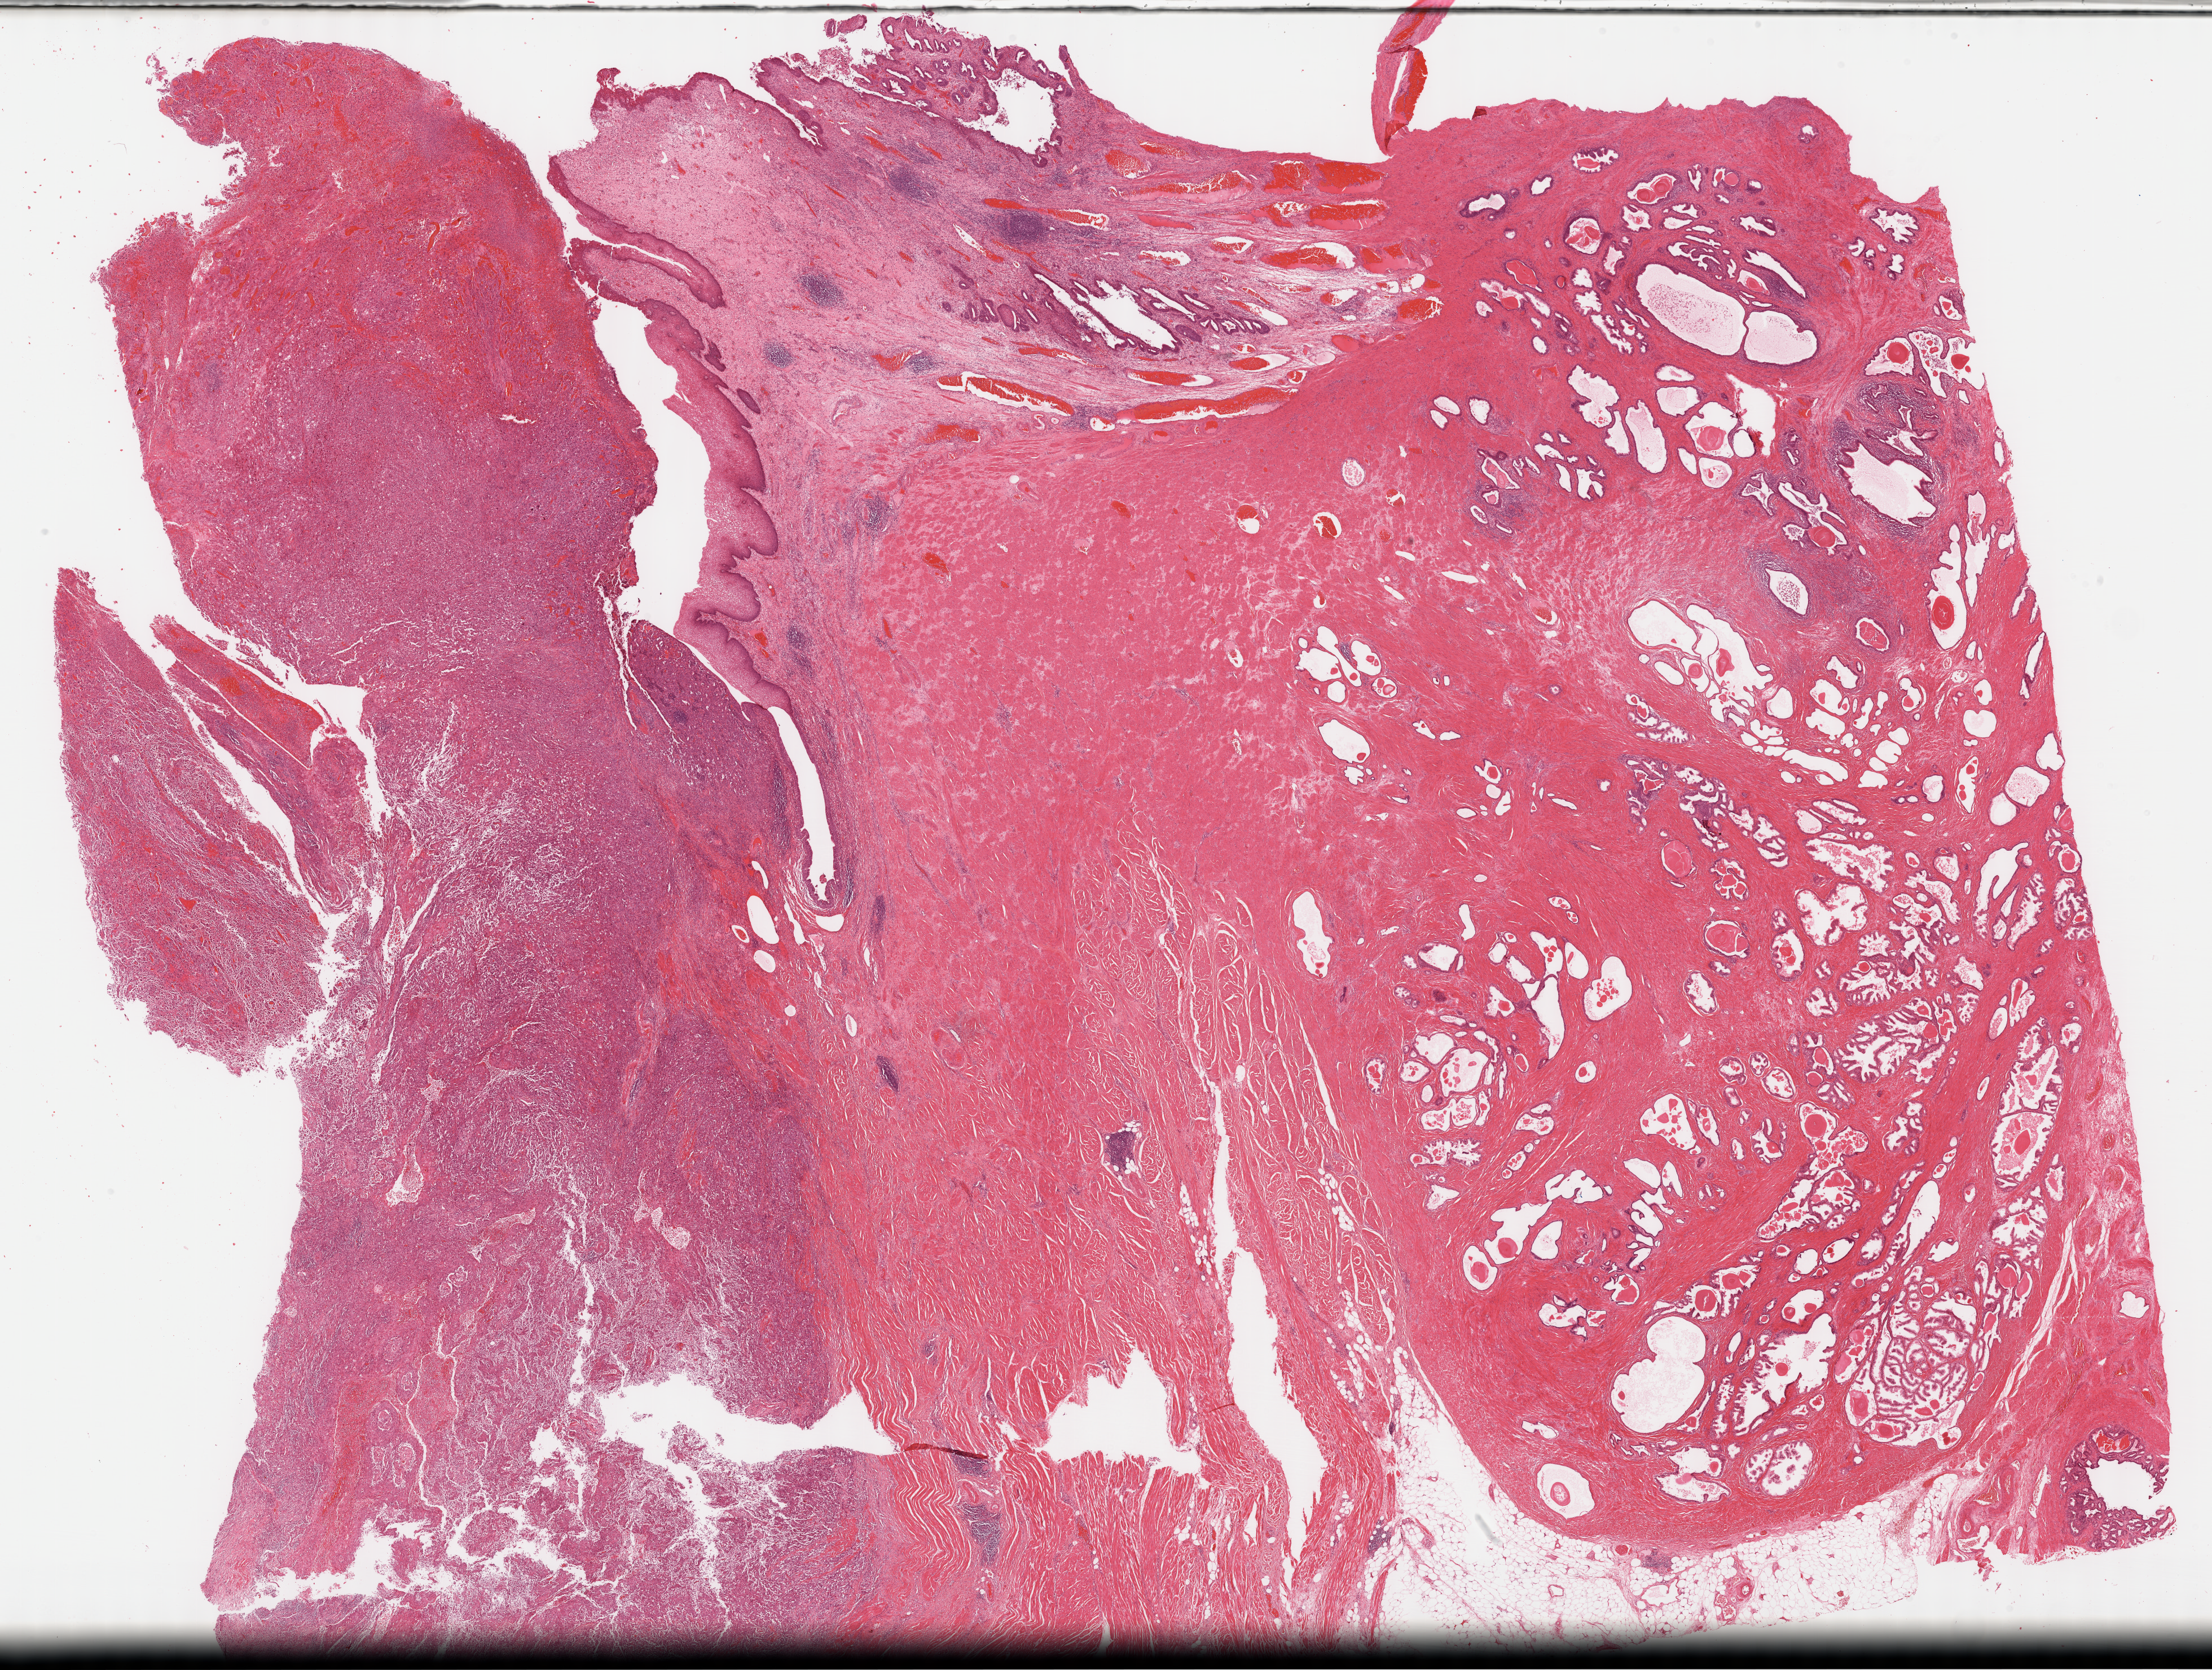
Digitized H&E-stained tissue section (whole slide) — low-resolution overview of the scanned area, about 31.7 x 23.9 mm, formalin-fixed paraffin-embedded (FFPE) diagnostic section, primary tumour sample from the bladder. Male, age 60 years at initial diagnosis. Histologic grade: high grade.
* AJCC pathologic stage: II (7th edition)
* histologic diagnosis: Transitional cell carcinoma